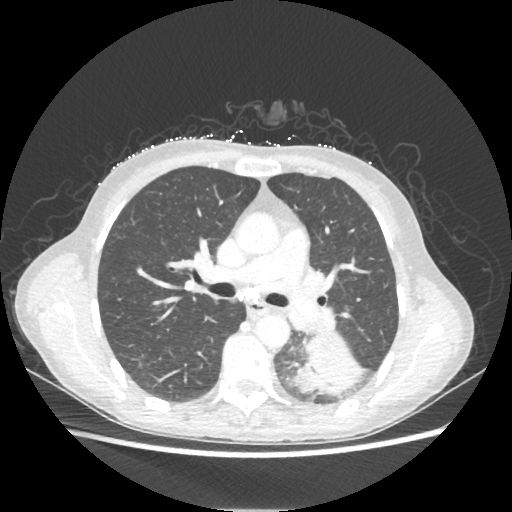
Chest CT, one axial slice; position 133 of 221 along the scan axis; 80 kVp; lung window (W 1500 / L -600 HU); 1.25 mm slice thickness; 512 × 512 image matrix, field of view 360 × 360 mm. Female patient, age 53 years. From the clinical record (not read from this slice): clinical TNM (as recorded): T3 N0 M0.
Outlined on this slice (rectangle marked by the reading radiologist):
- lung tumour (recorded histology: adenocarcinoma): bounding box (x1, y1, x2, y2) in pixels: (299, 324, 364, 393)